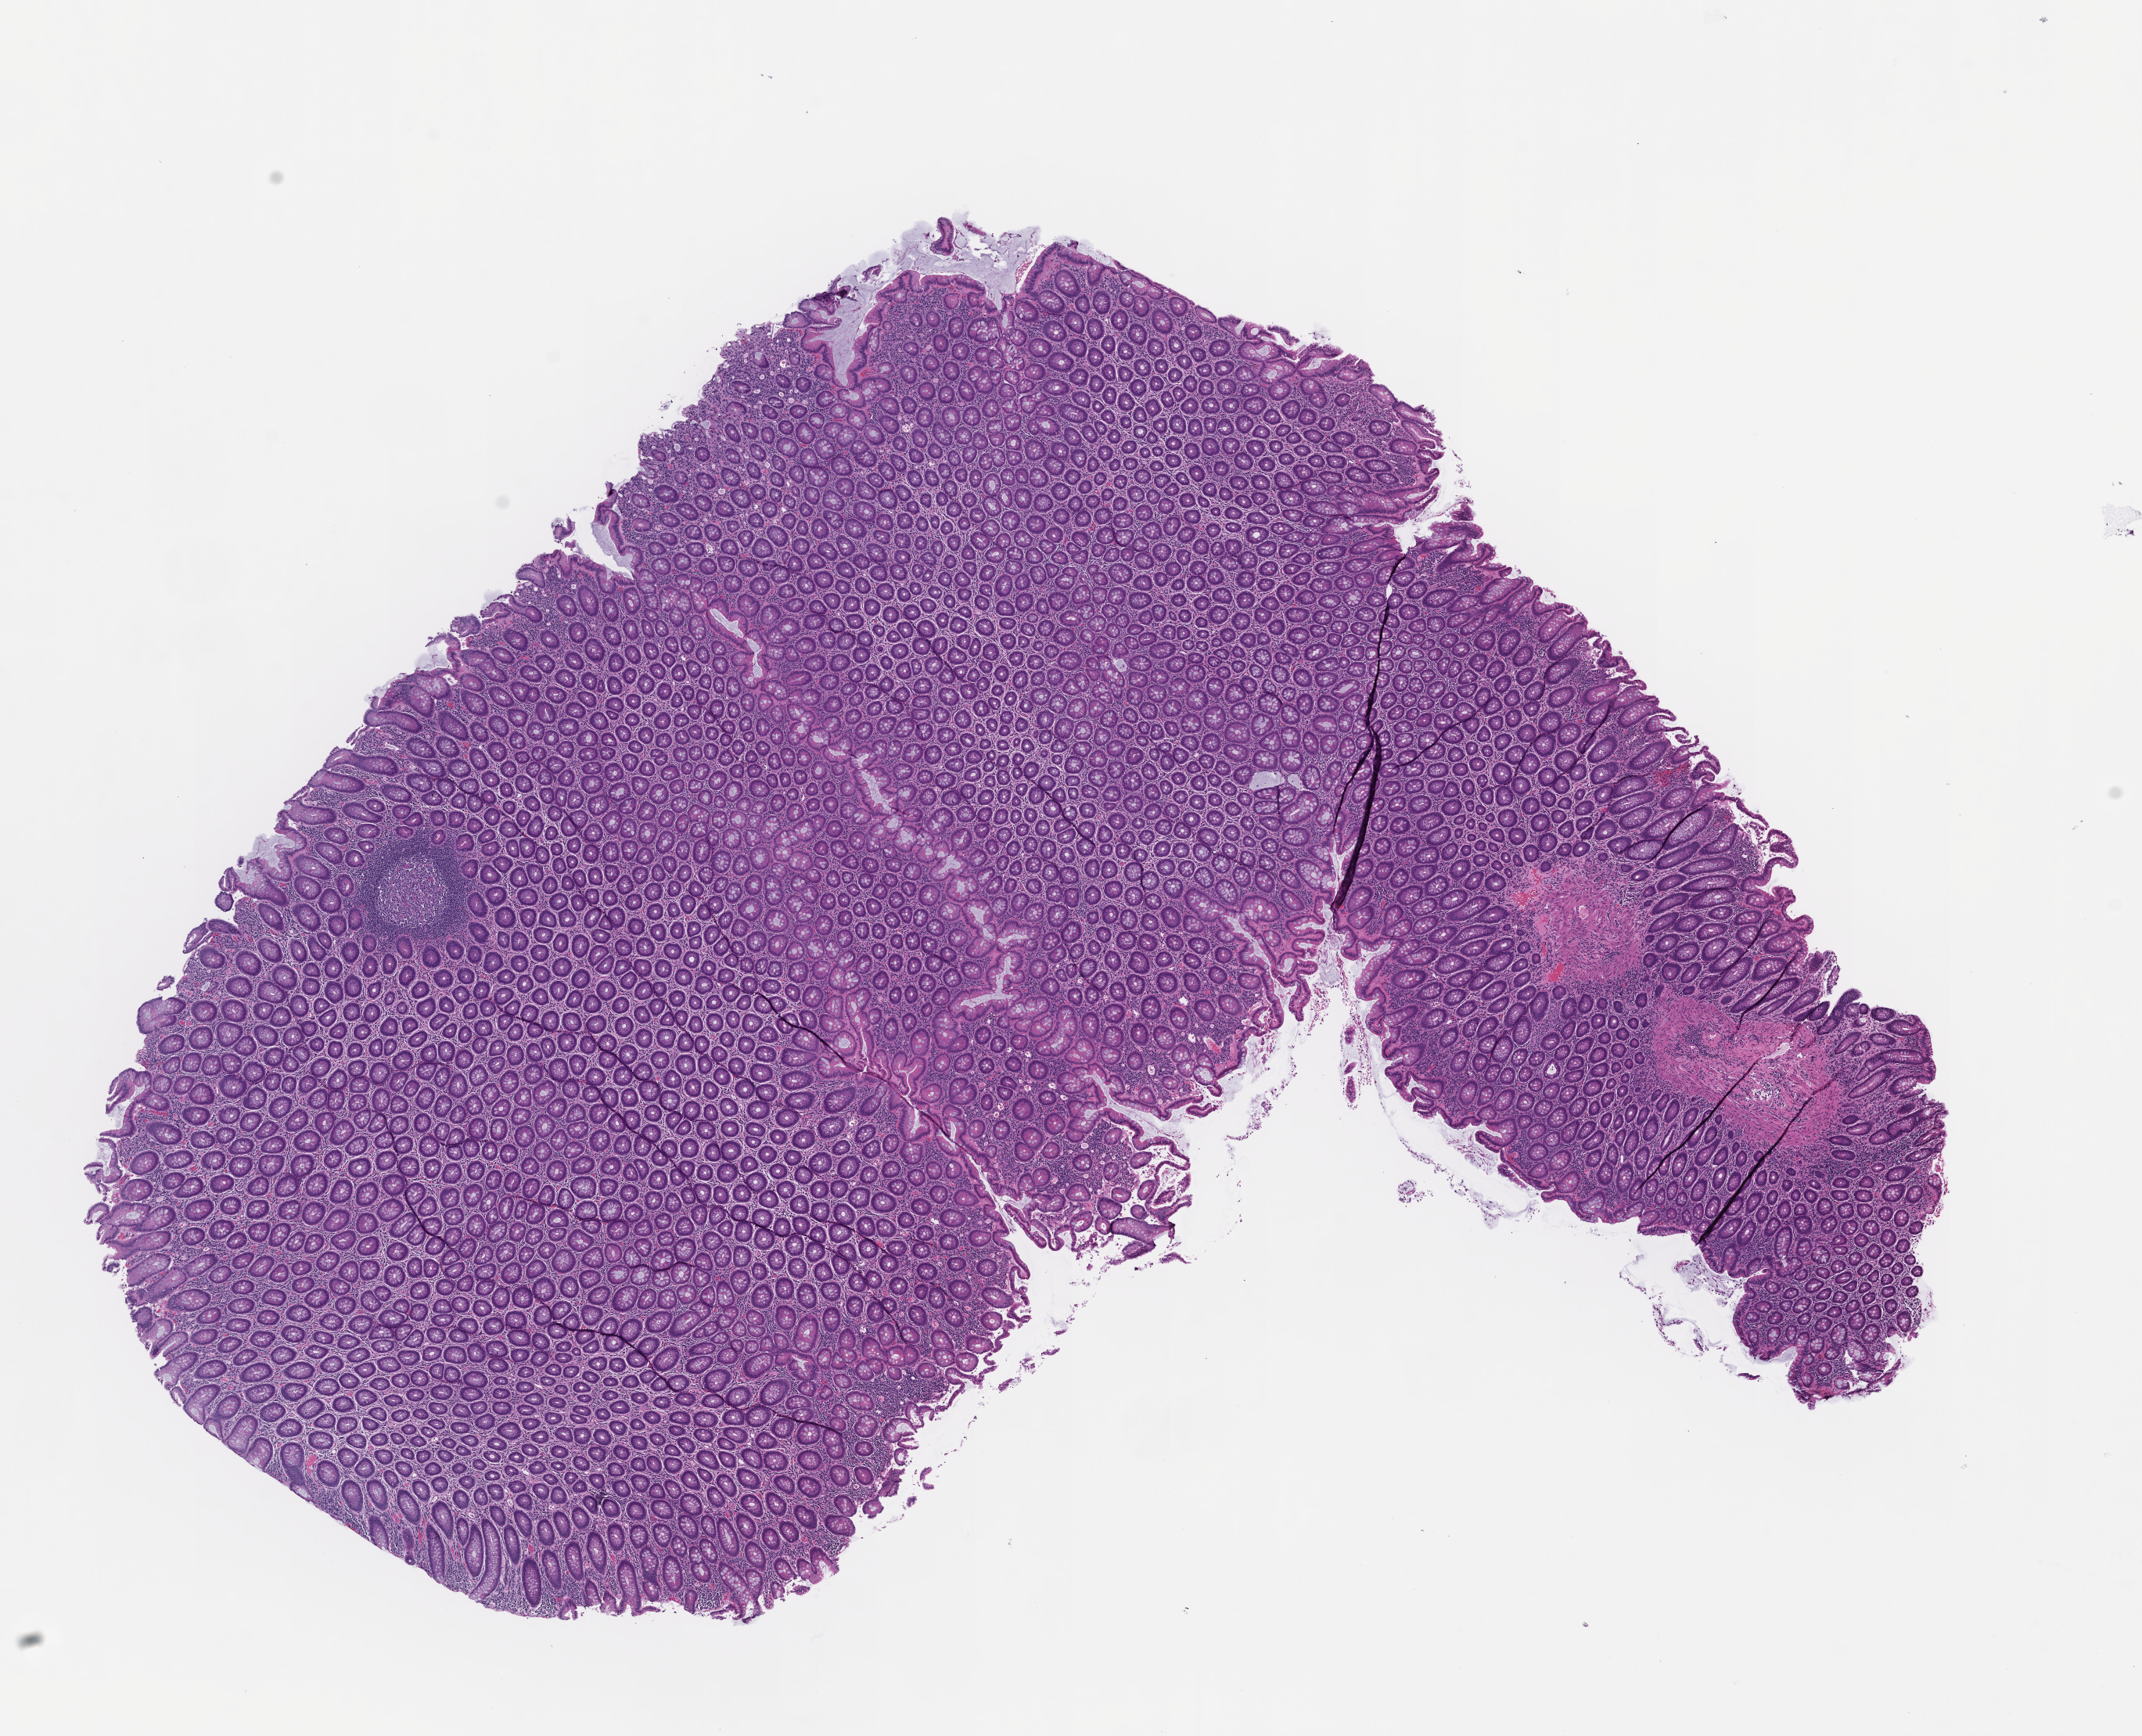
Whole-slide image, H&E stain, a low-resolution overview of the entire scanned area, about 11.1 x 9.0 mm; FFPE section; collected at baseline (before treatment). Patient sex: female.
This section: metastasis (sampled organ not recorded). Primary diagnosis of the patient: Colorectal Carcinoma.